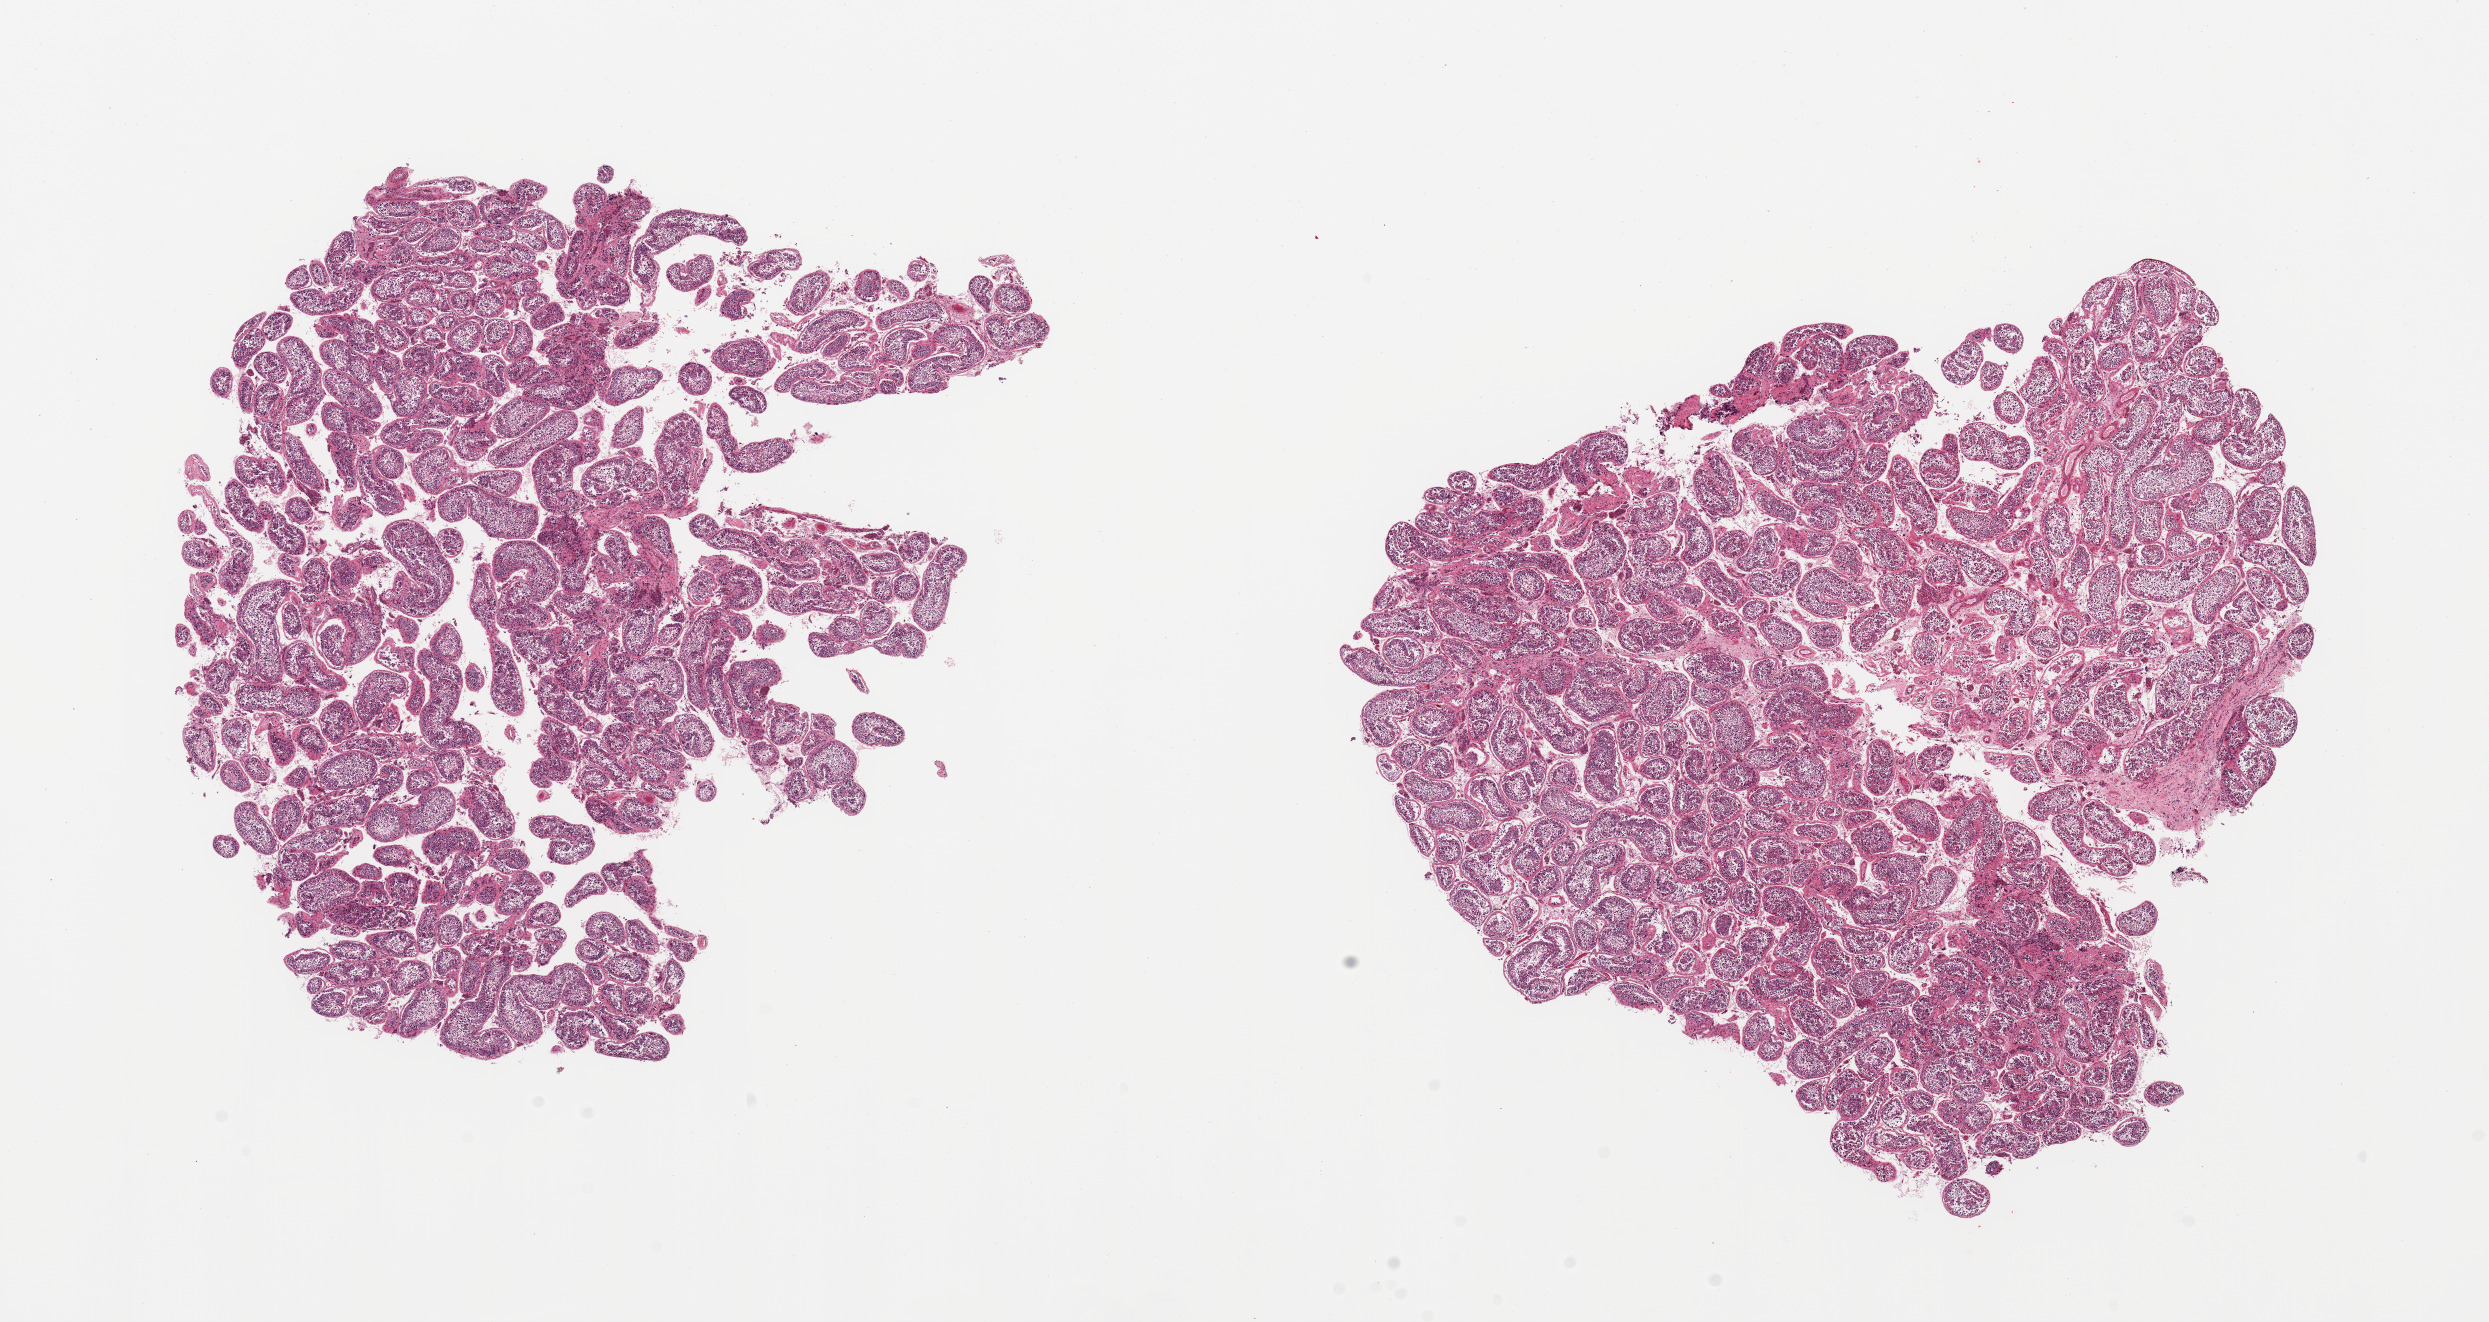
H&E whole-slide image, brightfield — a low-resolution overview of the entire scanned area, about 19.7 x 10.5 mm (slide scanned at 20x); PAXgene-fixed, paraffin-embedded tissue; sampled site (target tissue): testis; donor tissue sample.
- reviewer comment on this tissue sample: 2 pieces; spermatogenesis